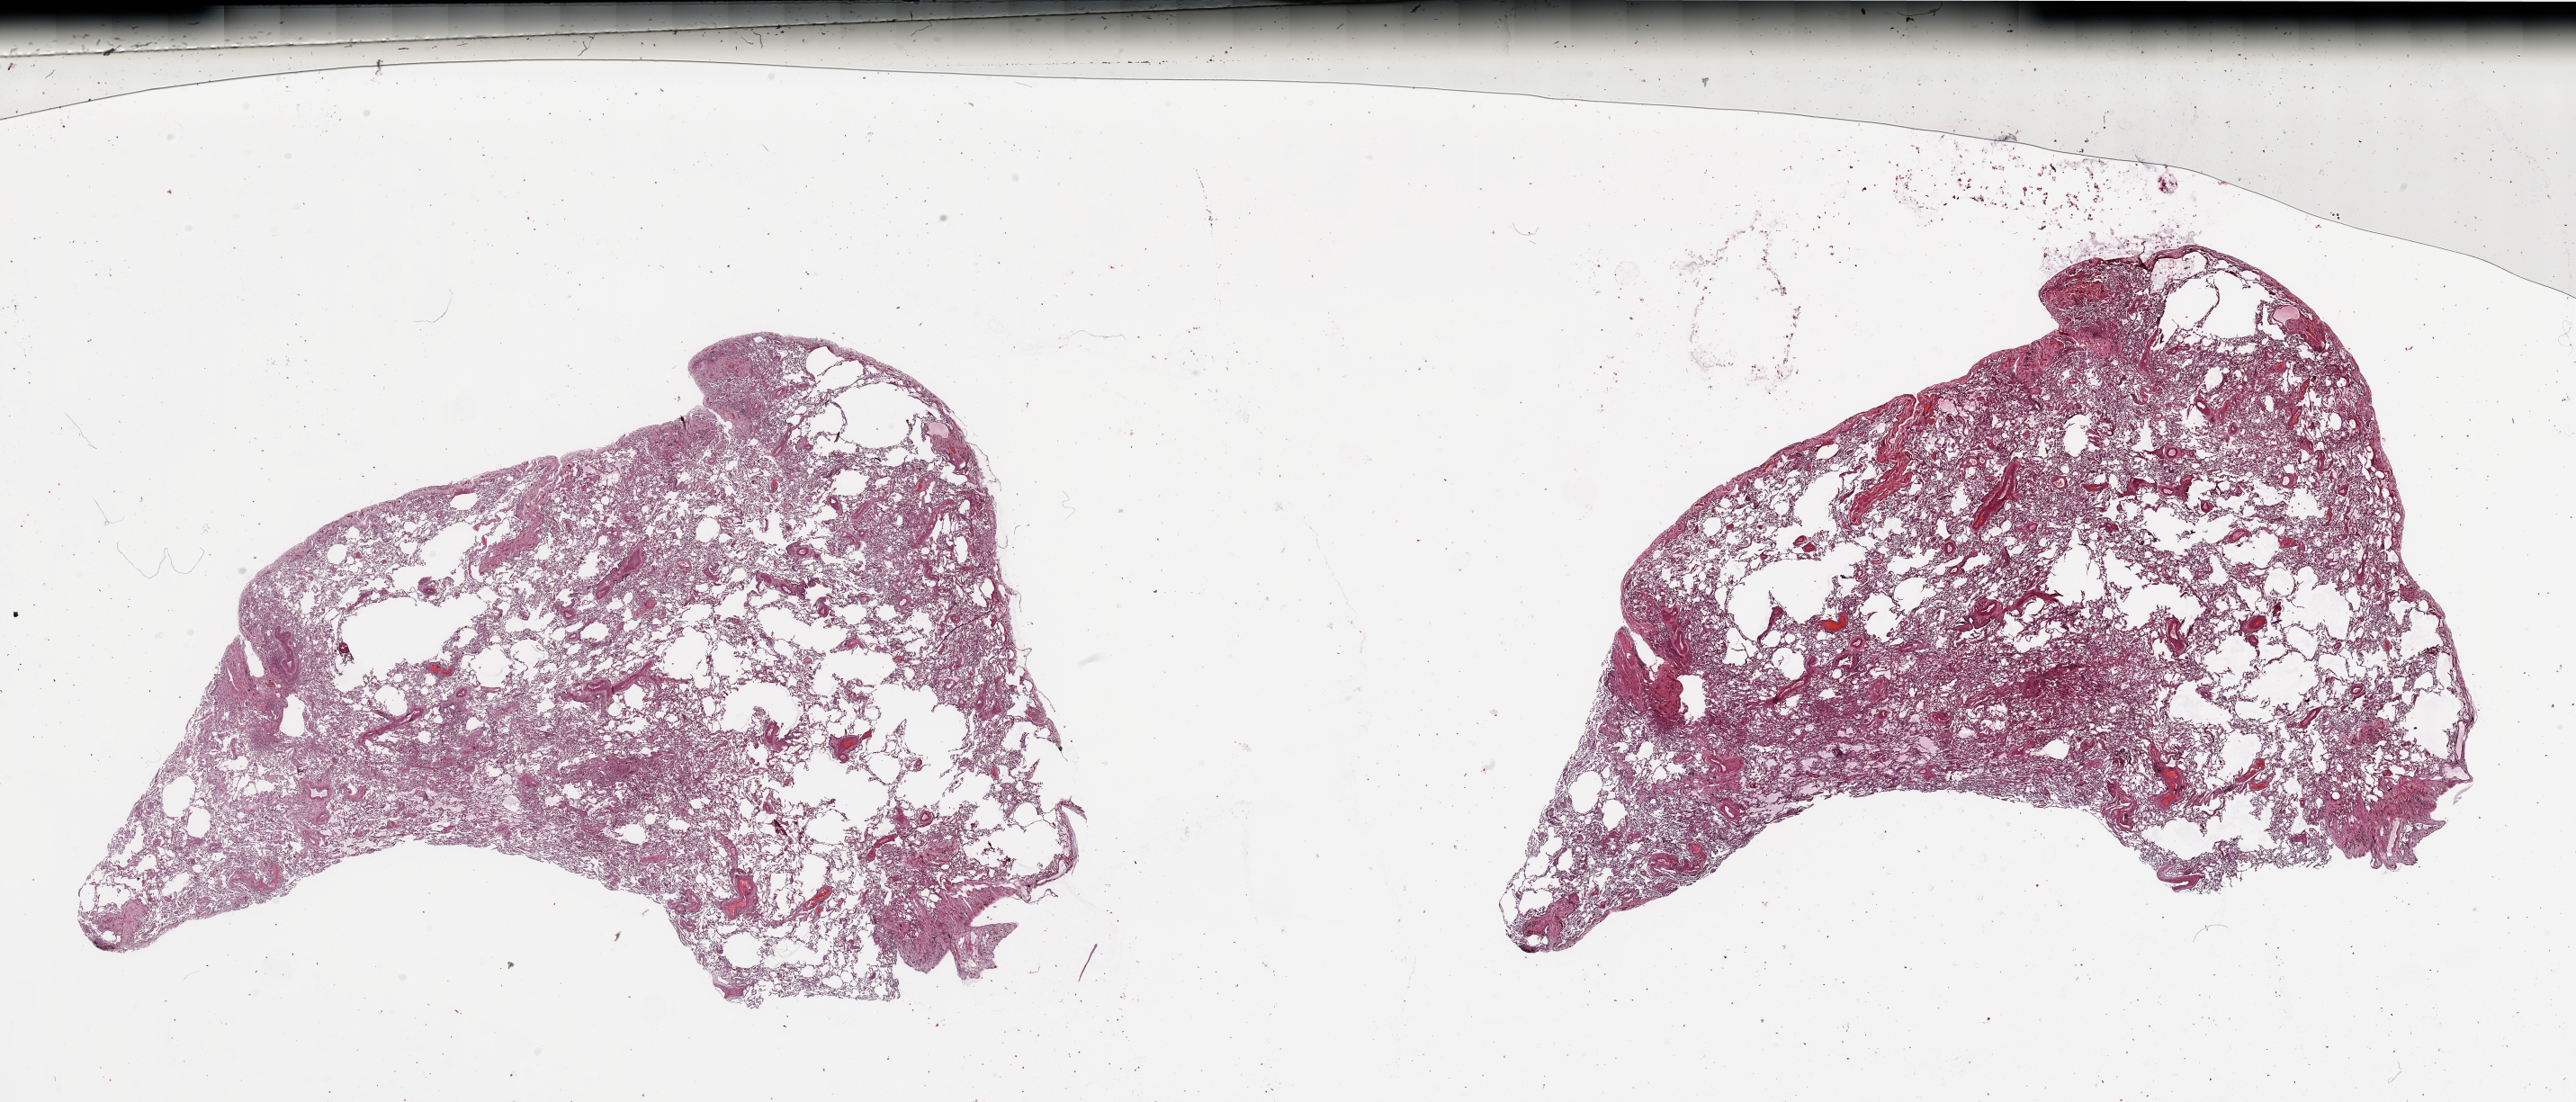
Digitized H&E tissue section (whole slide) — a low-resolution overview of the entire scanned area, about 45.3 x 19.4 mm (slide scanned at 20x), normal (non-tumour) tissue sample, lung. 74-year-old male patient.
This section: normal (non-tumour) tissue from the same patient. Patient diagnosis: Squamous cell carcinoma, NOS.